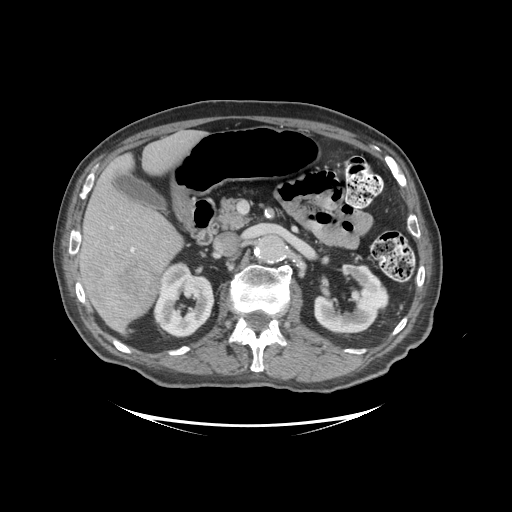
Contrast-enhanced abdominal CT (liver protocol), one axial slice. Slice 50 of 99 in the series (ordered by position). Reconstruction kernel STANDARD. 140 kVp. Soft-tissue window (W 400 / L 40 HU). 2.5 mm slice thickness. 512 × 512 image matrix, field of view 460 × 460 mm. Case-level facts recorded for this patient, not image findings: diagnosis: hepatocellular carcinoma (patient treated with transarterial chemoembolisation; whether this scan precedes or follows treatment is not stated here); TNM stage (as recorded): Stage-I; Child-Pugh class: A; tumour differentiation: moderately differentiated; tumour nodularity: uninodular.
Structures marked on this image (semi-automatic segmentation, software-assisted and operator-edited):
- liver parenchyma outside the tumour (the mass and vessels are separate outlines, so this box may not span the whole liver): box from (x=77, y=130) to (x=204, y=332) px
- mass: (x=86, y=258)–(x=160, y=320)
- liver vessels: (x=110, y=226)–(x=134, y=252)